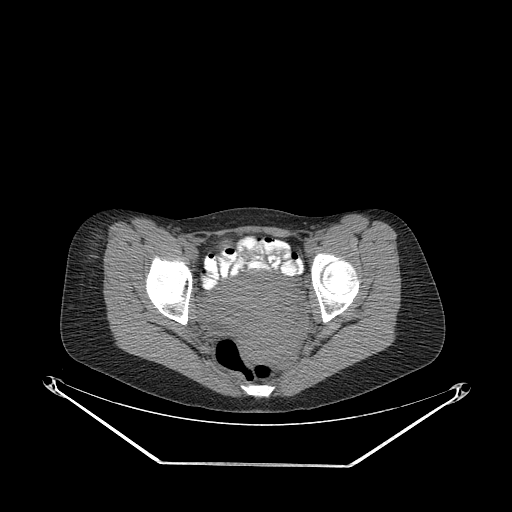
CT of an extremity soft-tissue mass (from a PET/CT study), one axial slice; position 72 of 267 along the scan axis; reconstruction kernel STANDARD; 140 kVp; soft-tissue window (W 400 / L 40 HU); 3.75 mm slice thickness; 512 × 512 image matrix, field of view 500 × 500 mm. Female patient. From the clinical record (not read from this slice): histological type: synovial sarcoma; grade: intermediate; site of the primary tumour: right thigh.
Outlined on this slice (expert contour drawn on MRI and transferred to this co-registered scan by the dataset authors):
- gross tumour volume including surrounding oedema: bounding box <87,237,104,263> (left, top, right, bottom; pixels)
- gross tumour volume (mass): <87,242,101,263>